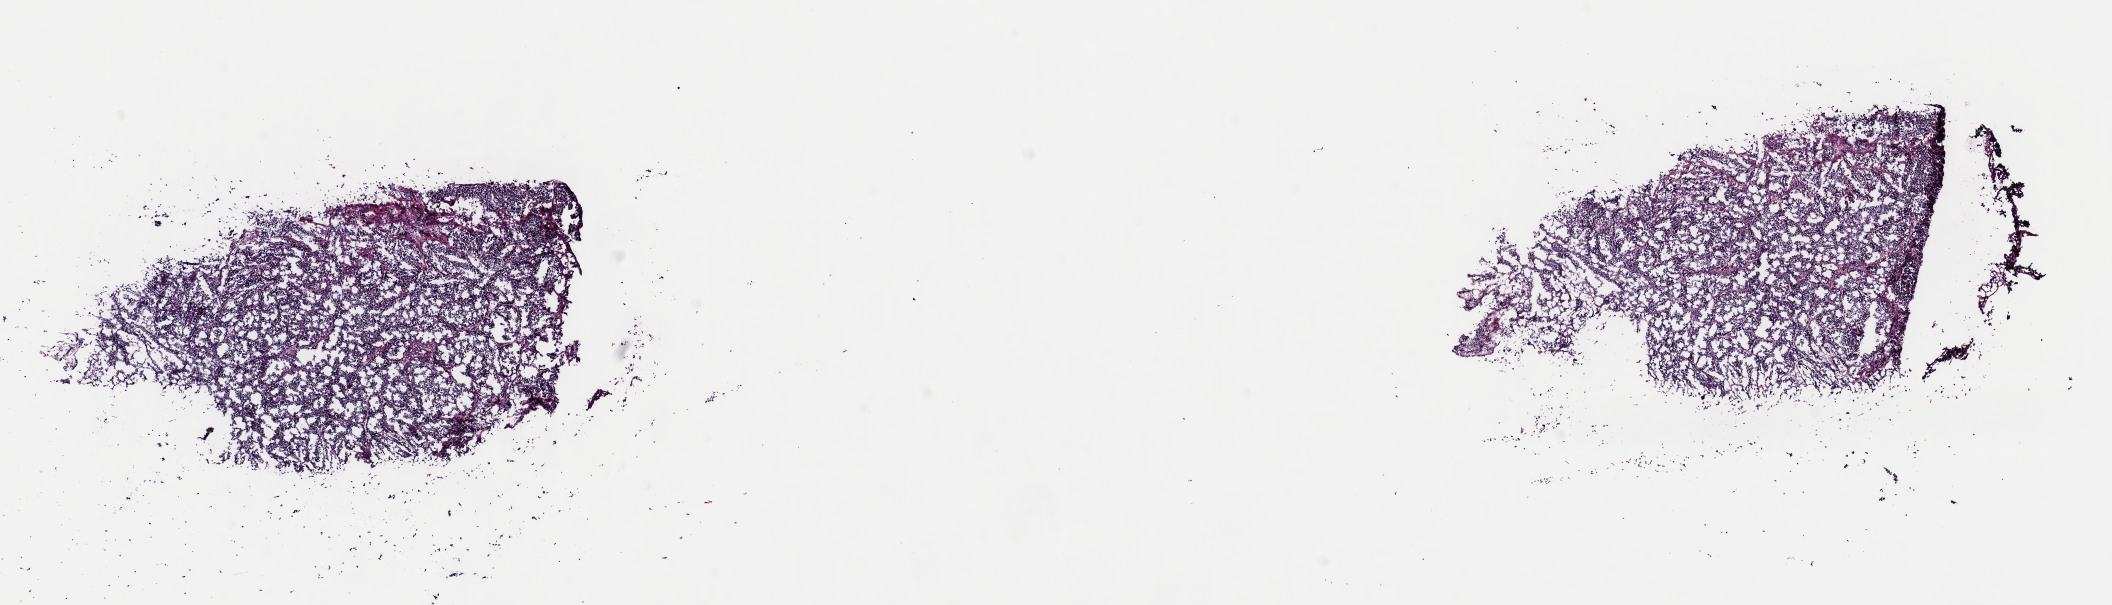
H&E-stained whole-slide image — whole scanned area (about 16.7 x 4.8 mm, acquisition: 40x scan) shown as a low-resolution overview, frozen section from the top of the tissue portion, bladder, primary tumour sample. Patient: male, age at initial diagnosis 73 years. Histologic grade: high grade. Pathologist review of this section (percent, as recorded): tumour cells 85%, tumour nuclei 85%, normal cells 0%, stromal cells 15%, necrosis 0%. Infiltration values recorded for this section: lymphocyte infiltration 2%, monocyte infiltration 0%, neutrophil infiltration 0%.
AJCC pathologic stage: III. Histologic diagnosis: Transitional cell carcinoma (ureteric orifice). Lymph nodes positive (case pathology): 0 of 57 examined.